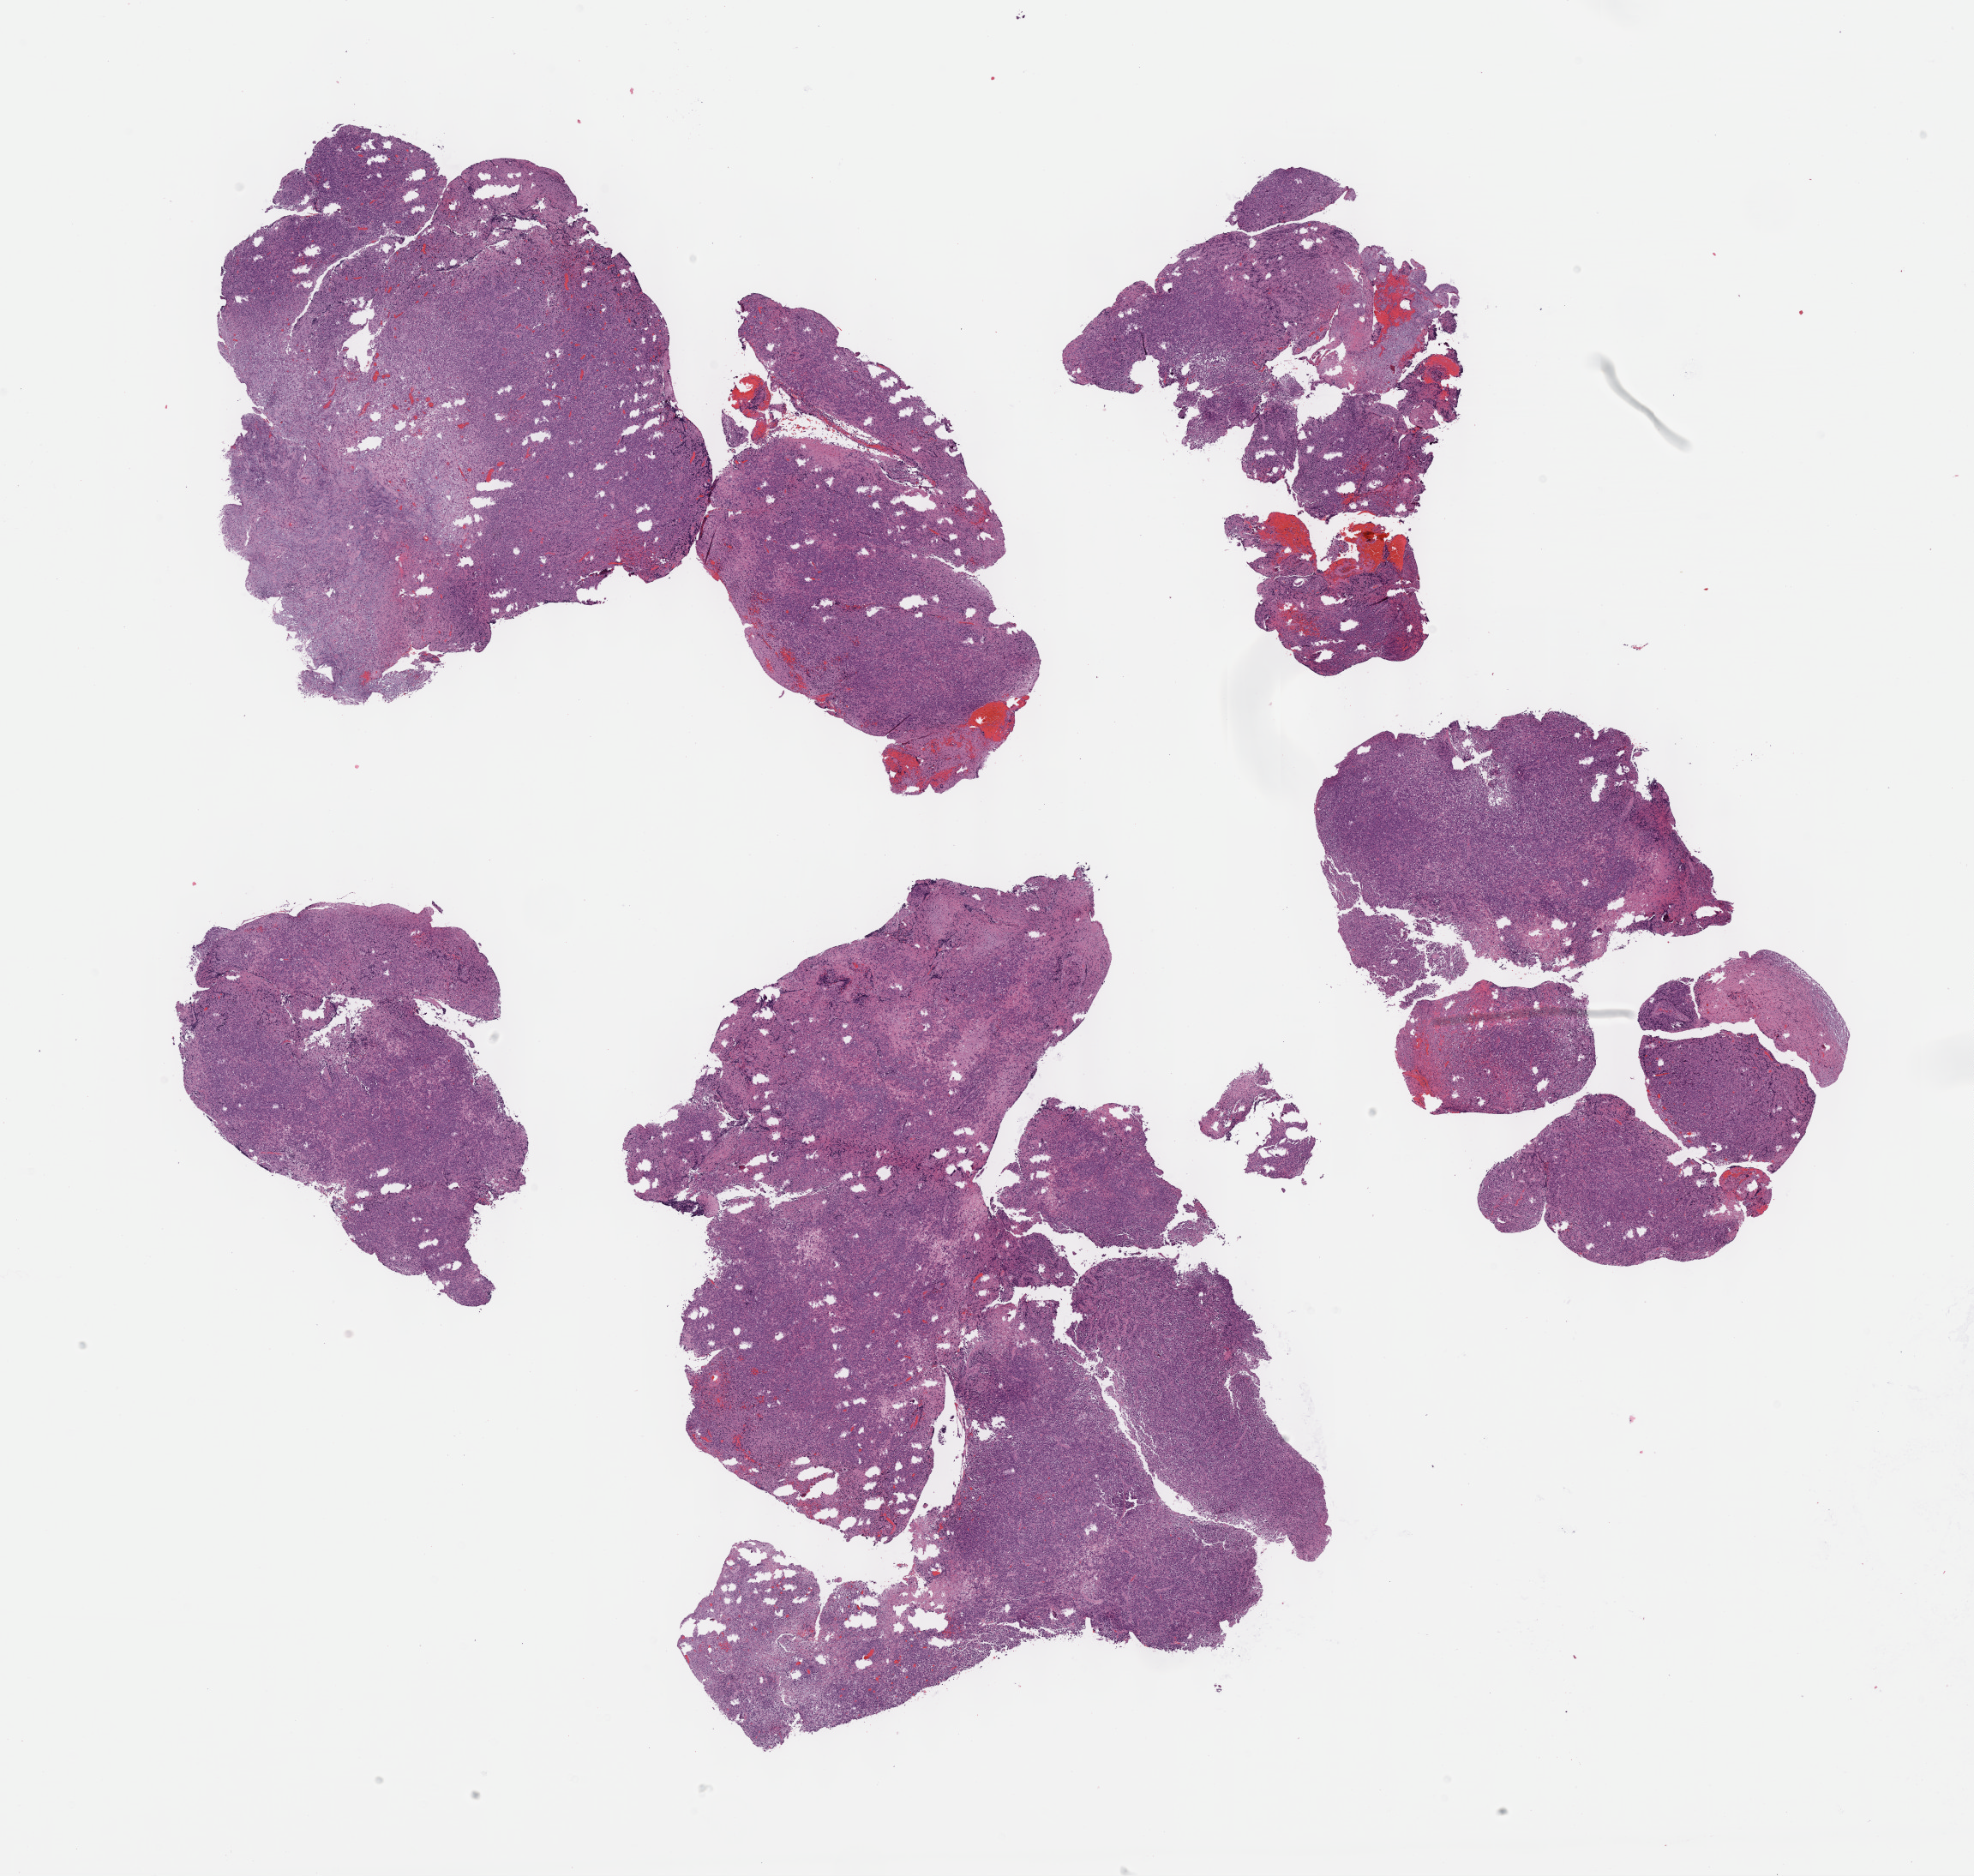
Digitized H&E-stained tissue section (whole slide) — a low-resolution overview of the entire scanned area, about 18.6 x 17.7 mm; formalin-fixed paraffin-embedded (FFPE) diagnostic section; sample: primary tumour, lymphoid tissue. Male, age 63 years at initial diagnosis.
• pathologic diagnosis: Primary diffuse large B-cell lymphoma of the CNS (brain stem)